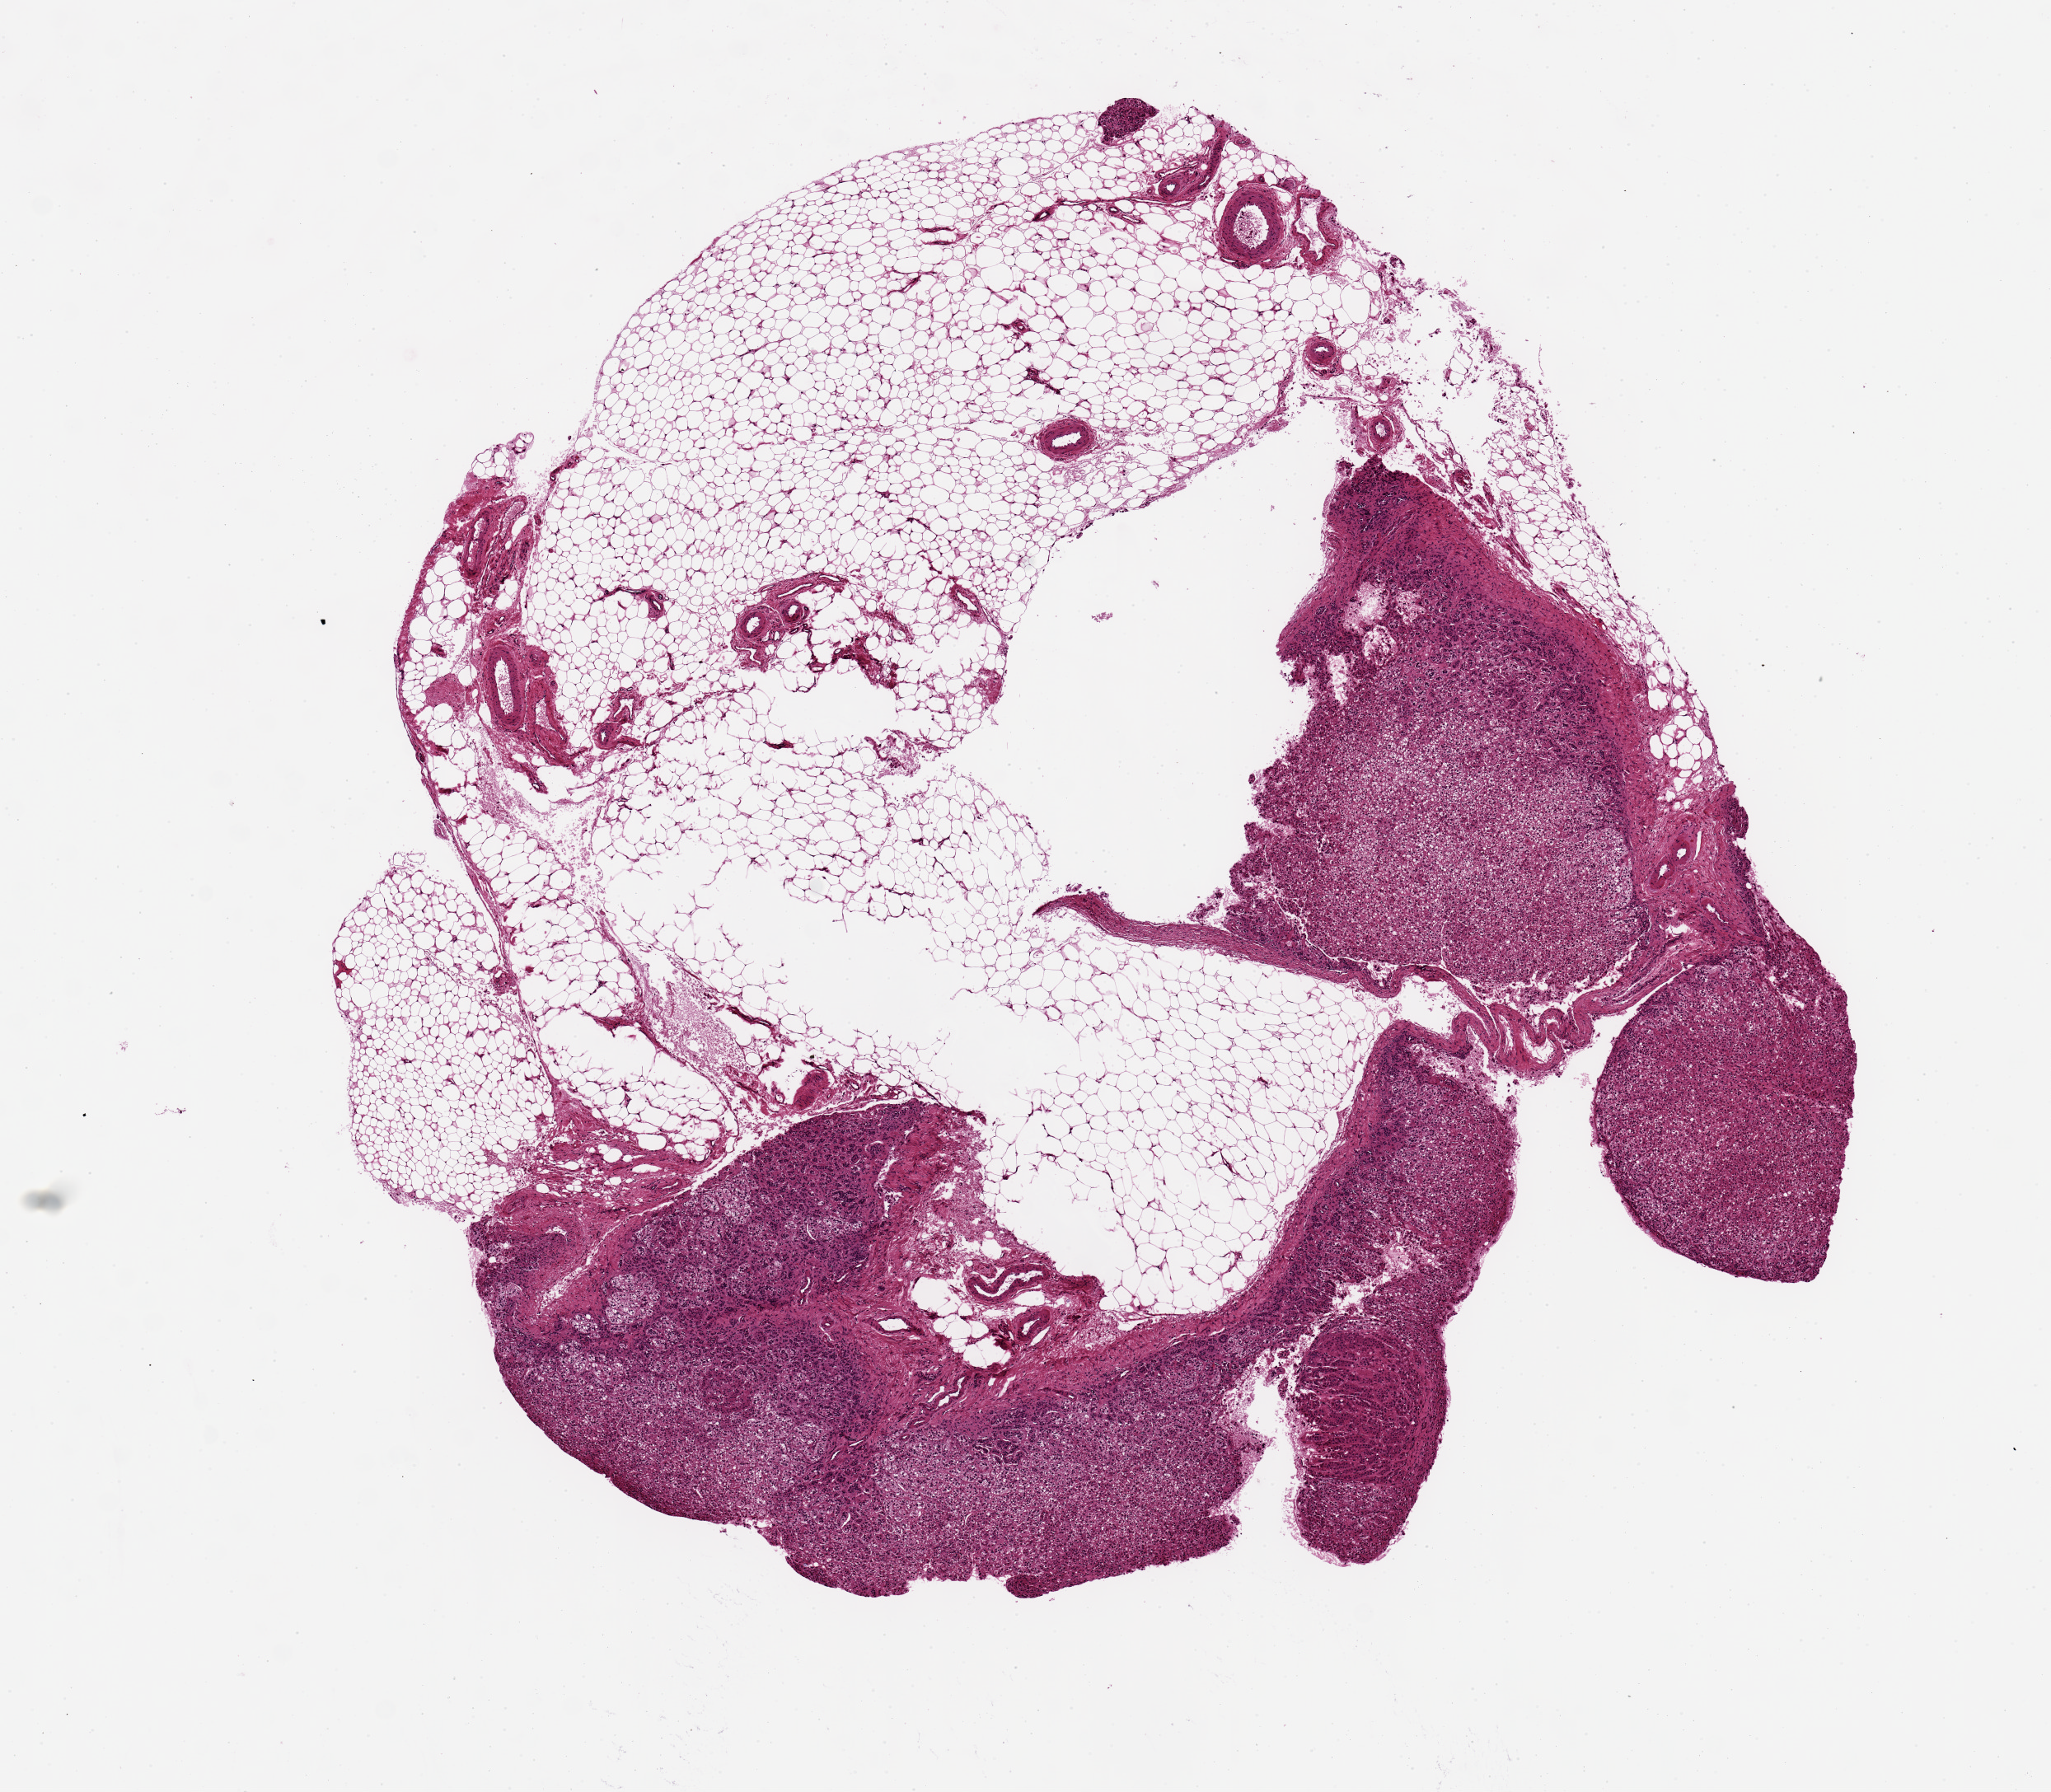
Whole-slide image, hematoxylin and eosin (H&E) stain, brightfield — whole scanned area (about 9.8 x 8.6 mm, acquisition: 20x scan) shown as a low-resolution overview; PAXgene-fixed paraffin-embedded (PFPE) section; target tissue: adrenal gland; tissue donor sample. Donor: male.
Reviewer comment on this tissue sample: All cortex, OK for analysis.